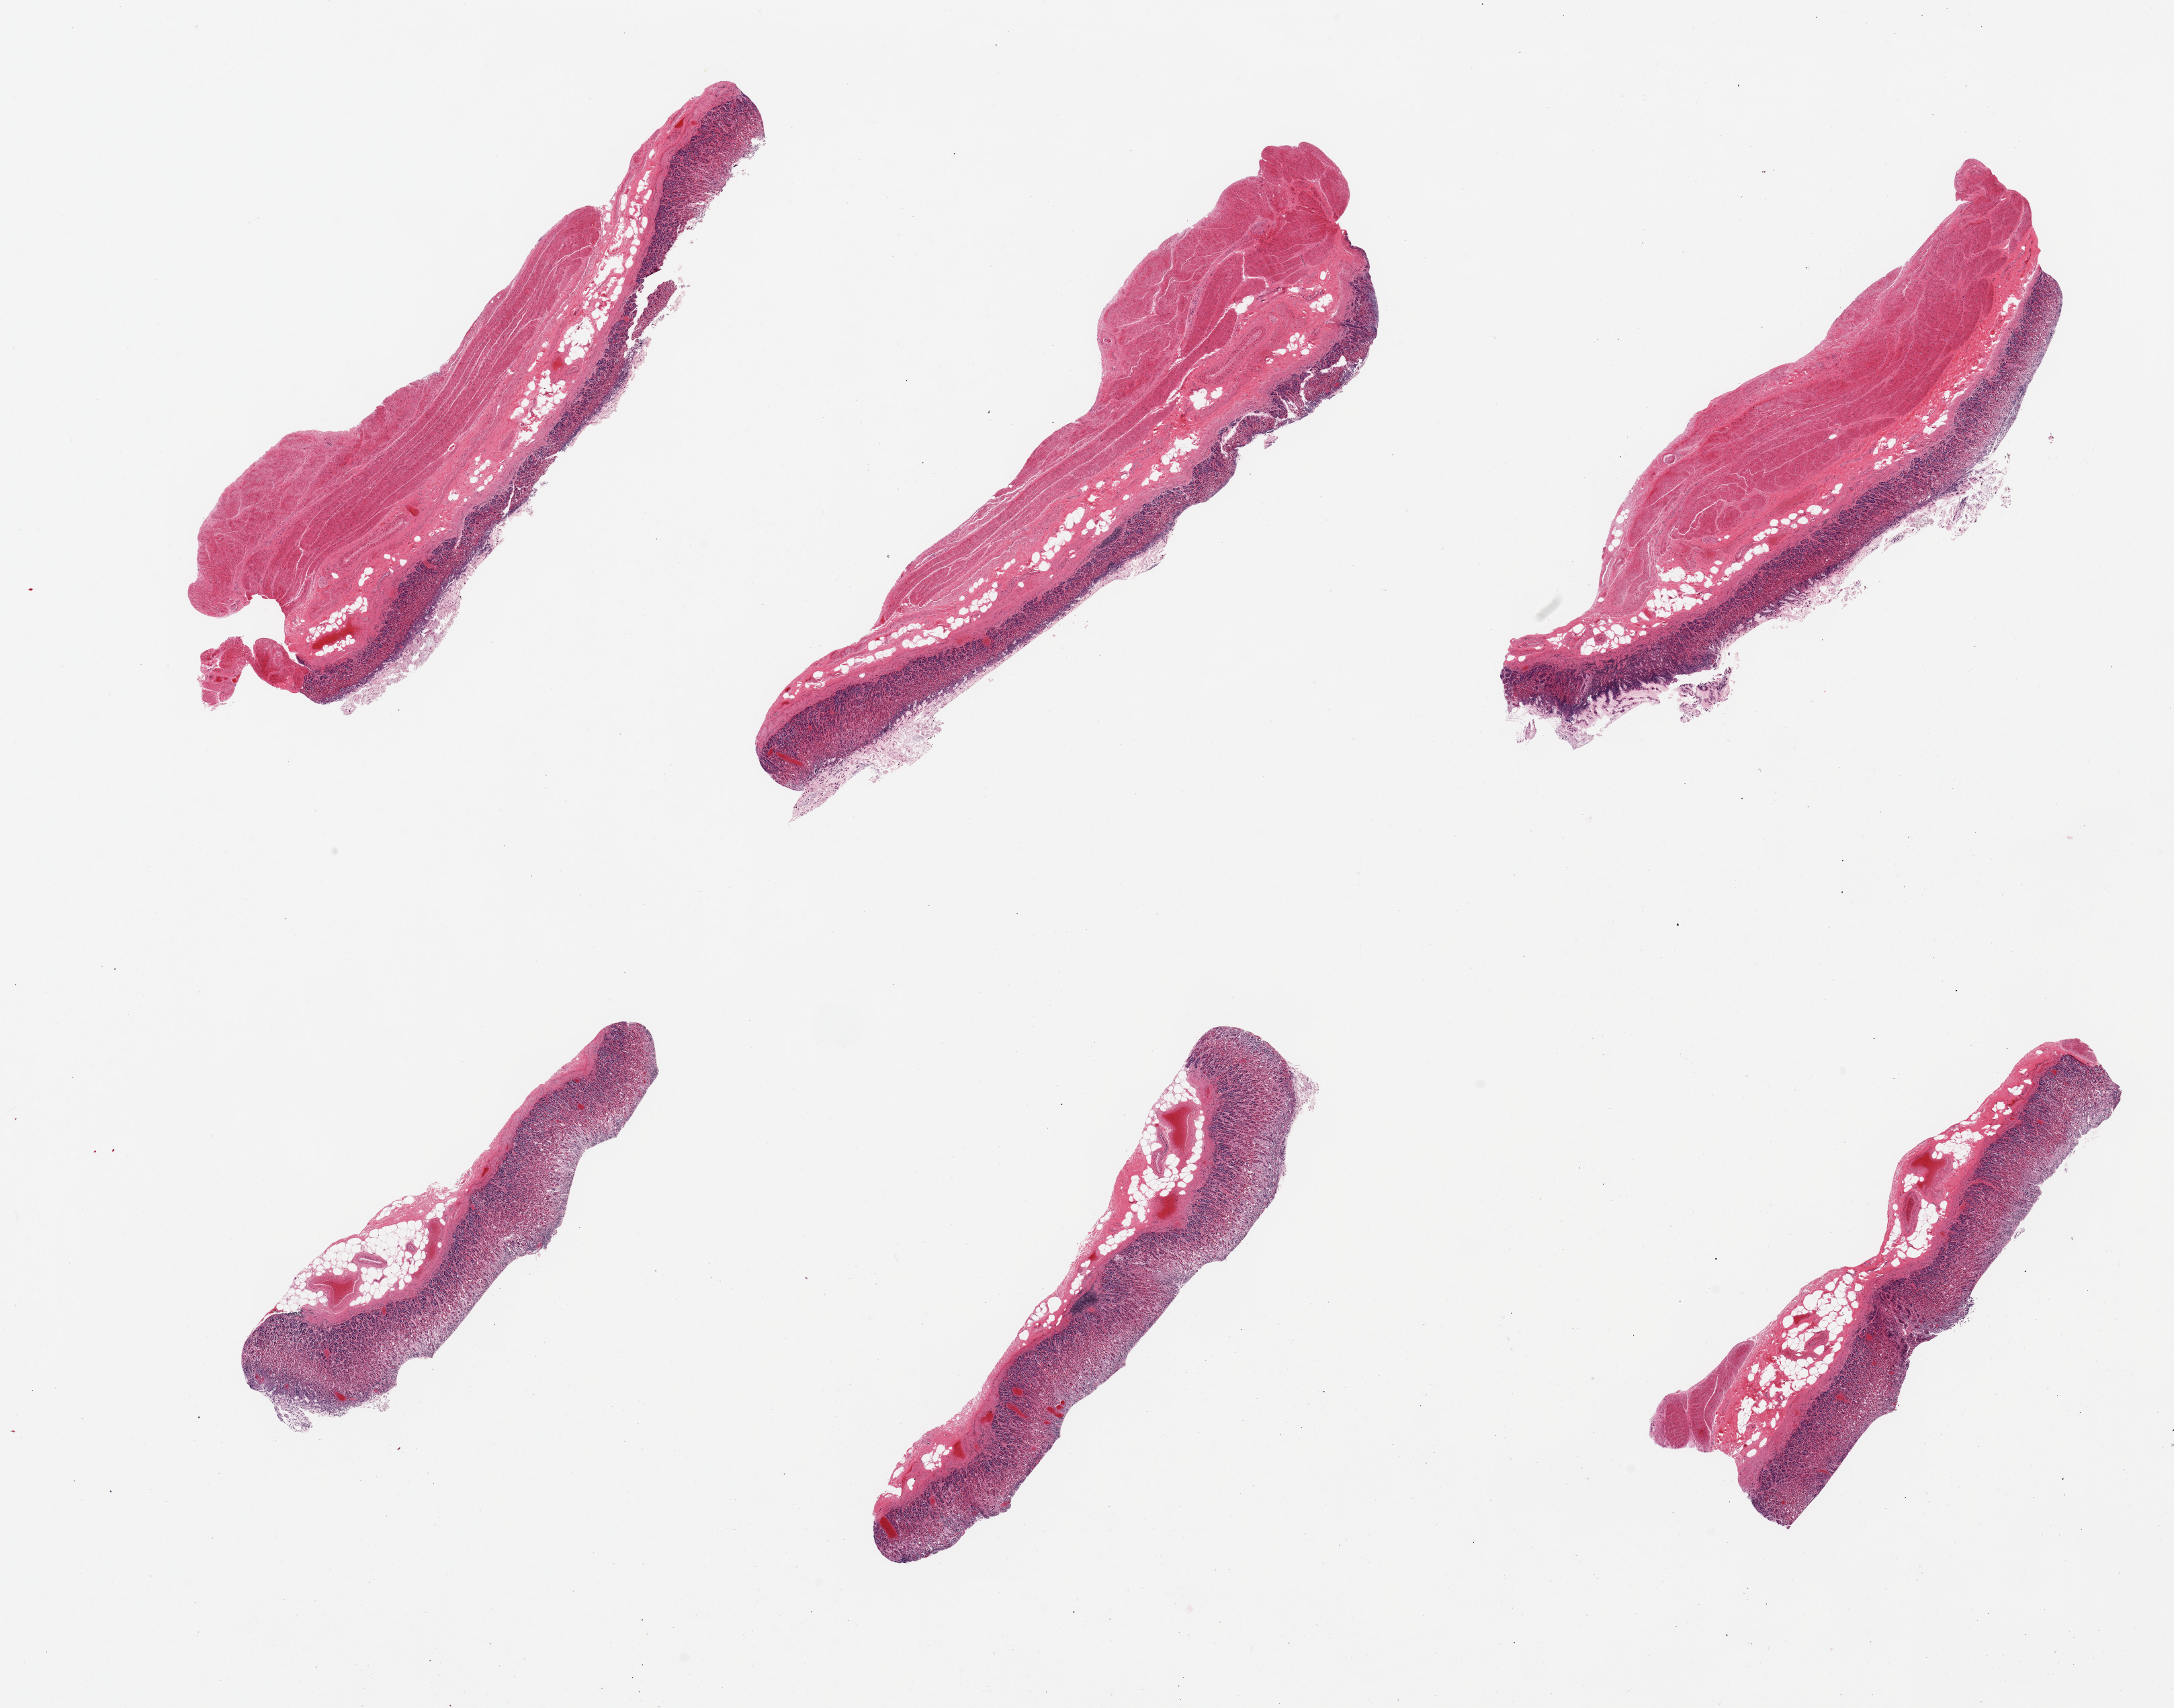
Whole-slide image, H&E stain, whole scanned area (about 25.6 x 20.1 mm, from a 20x scan) shown as a low-resolution overview, PAXgene-fixed paraffin-embedded (PFPE) section, section of stomach (target tissue), tissue donor sample.
Reviewer comment on this tissue sample: 6 pieces; 3 have mucosa only.